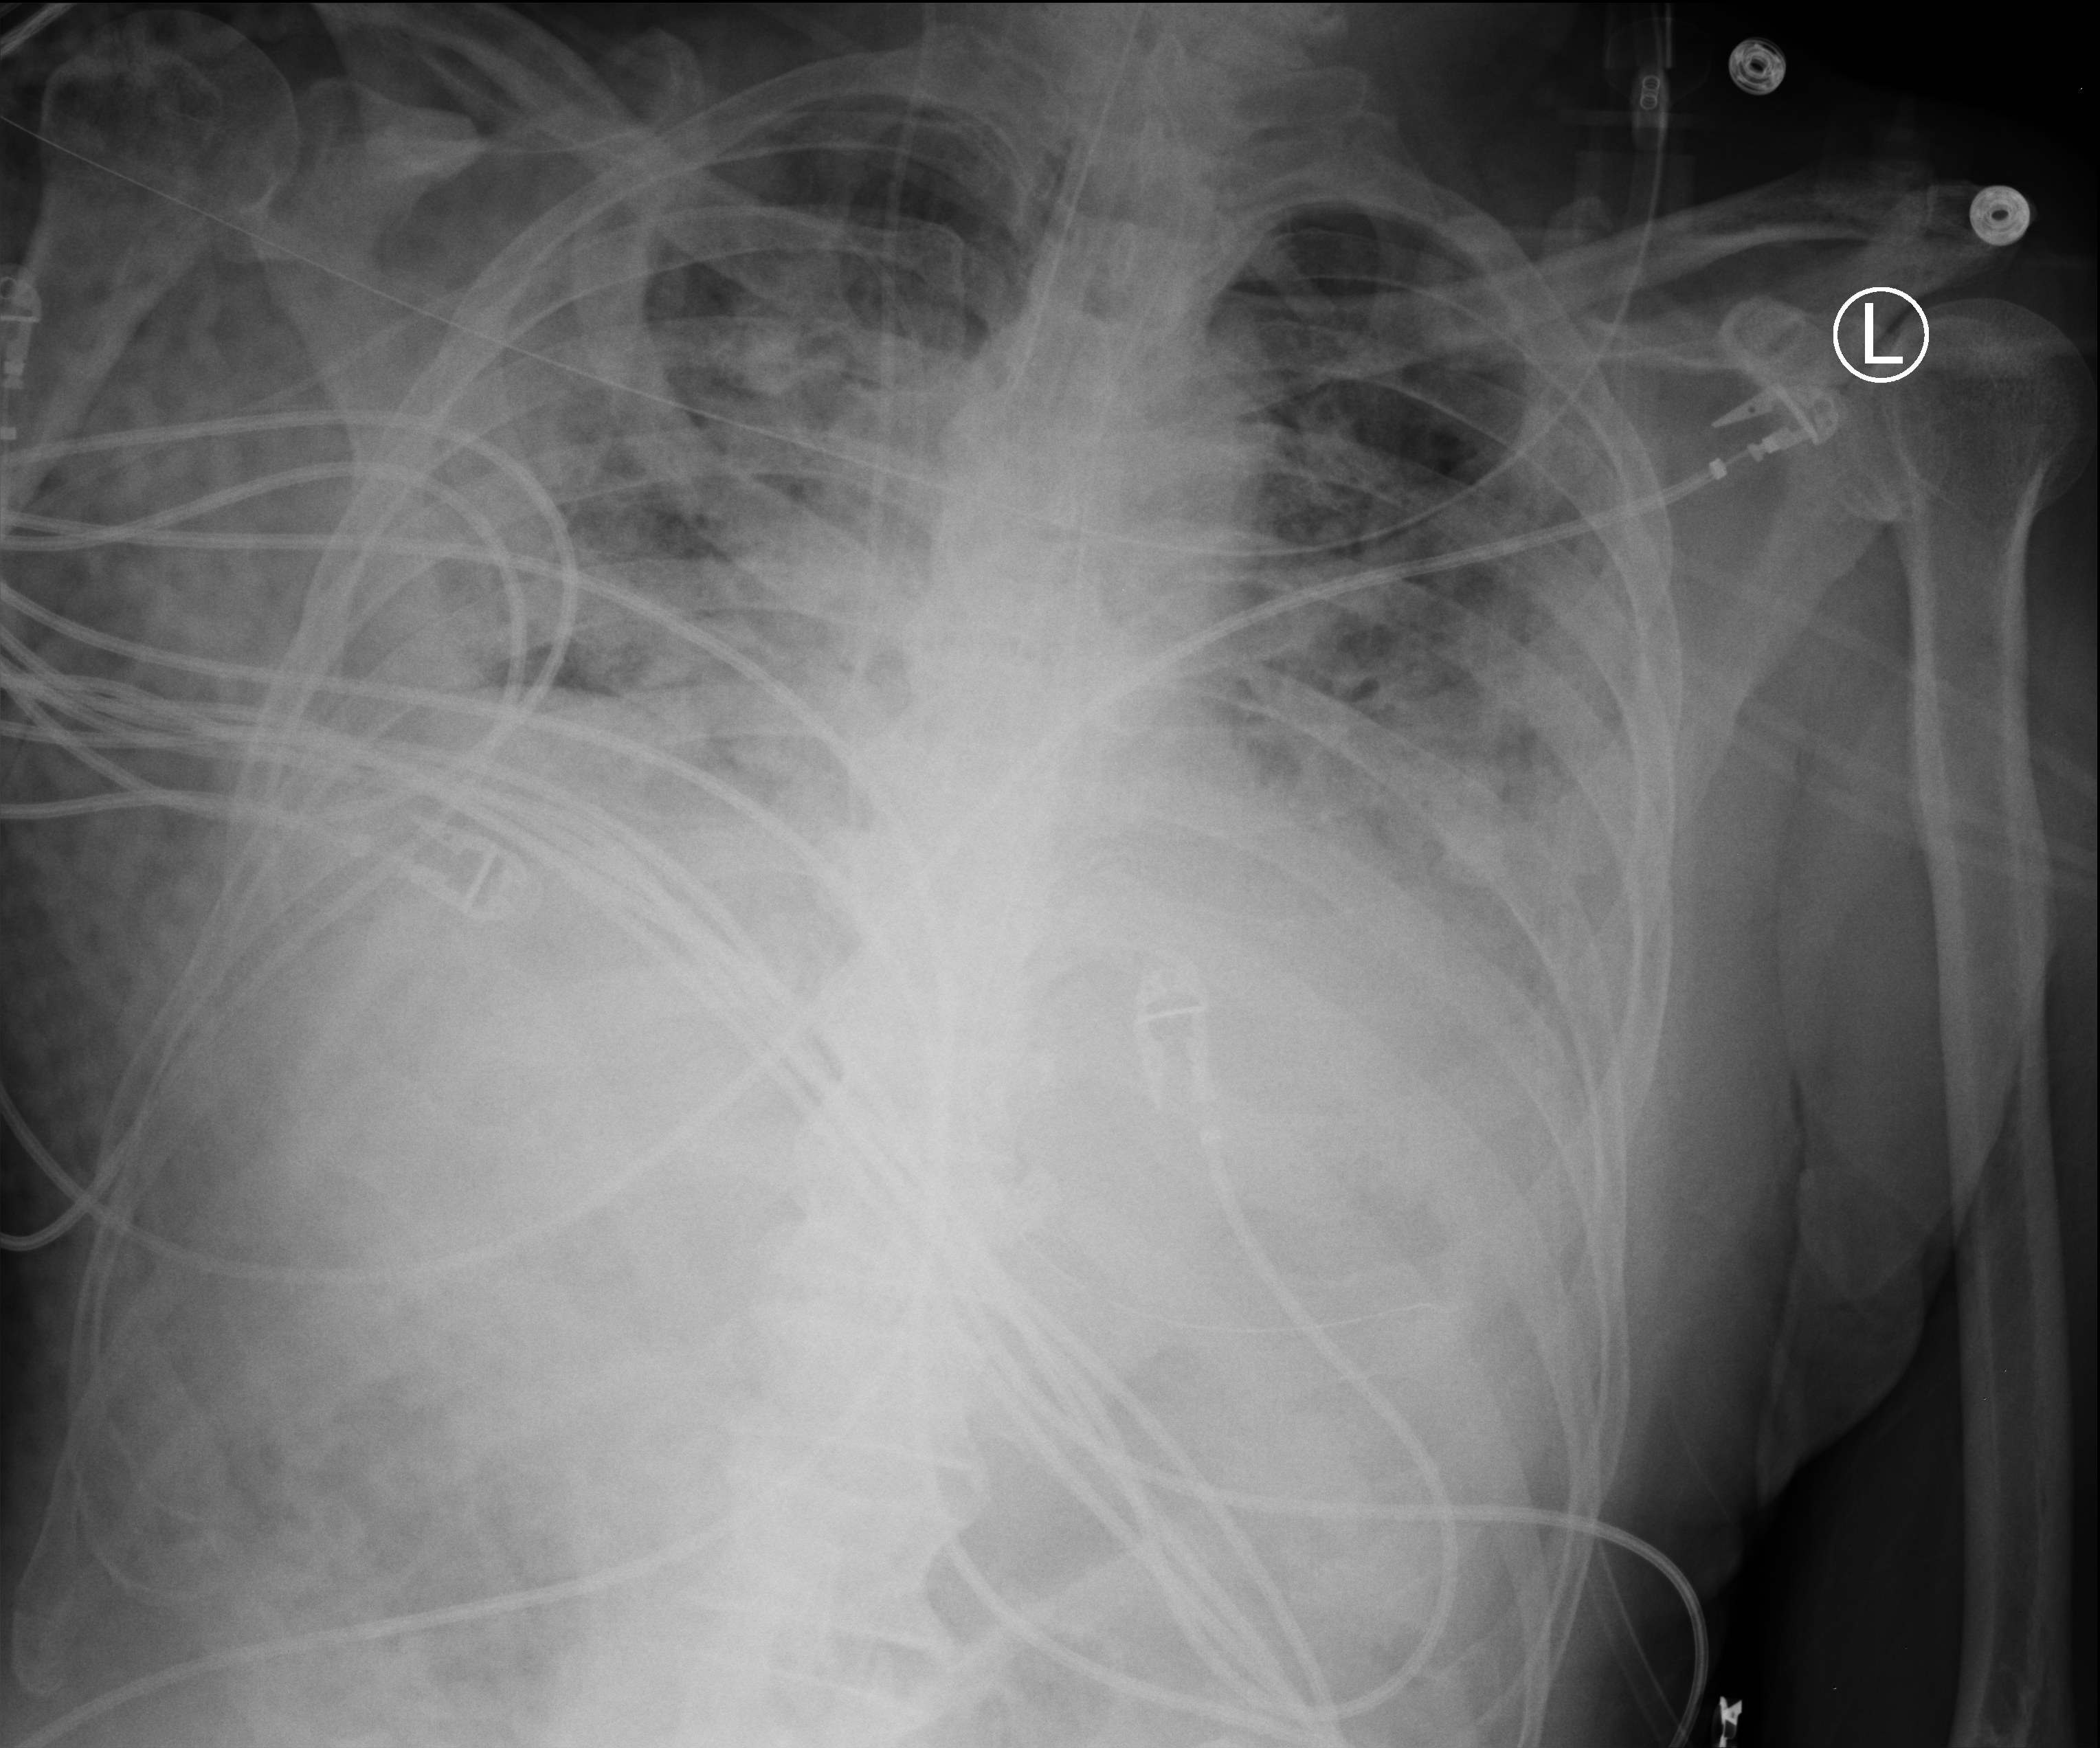
Portable chest radiograph, anteroposterior (AP) projection. Patient hospitalised with COVID-19; male, aged 75–90 years.
Hospital-stay facts (about this admission, not read from this image; timing relative to this image not recorded): length of hospital stay: 33 days.